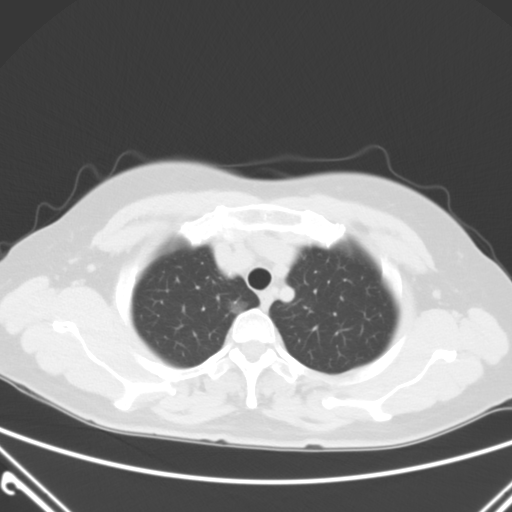
Chest CT, one axial slice; position 48 of 60 along the scan axis; 120 kVp; lung window (W 1500 / L -600 HU); 512 × 512 image matrix, field of view 350 × 350 mm. Patient: female, 54 years. From the clinical record (not read from this slice): clinical TNM (as recorded): T1a N0 M0.
Outlined on this slice (rectangle marked by the reading radiologist):
- lung tumour (recorded histology: adenocarcinoma): box from (x=223, y=298) to (x=252, y=323) px